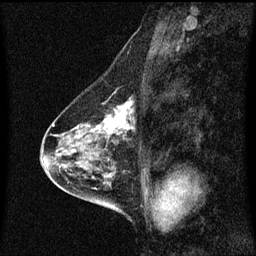
Breast MRI (dynamic contrast-enhanced), one sagittal slice. Position 28 of 60 along the scan axis. Dynamic contrast-enhanced series, image 2 of 3 at this slice position (ordered by acquisition). 1.5 T. TE 4.2 ms, TR 8.4 ms. 2 mm slice thickness. 256 × 256 image matrix, field of view 200 × 200 mm. Patient: female, 58 years.
Outlined on this slice (semi-automatic segmentation, software-assisted and operator-edited):
- analysis volume of interest (the breast-tissue region the enhancement analysis was run in; not a lesion): bounding box (x1, y1, x2, y2) in pixels: (86, 92, 136, 143)
- tumour enhancement mask (voxels above the 70 % enhancement threshold inside the analysis volume of interest): (86, 100, 134, 139)